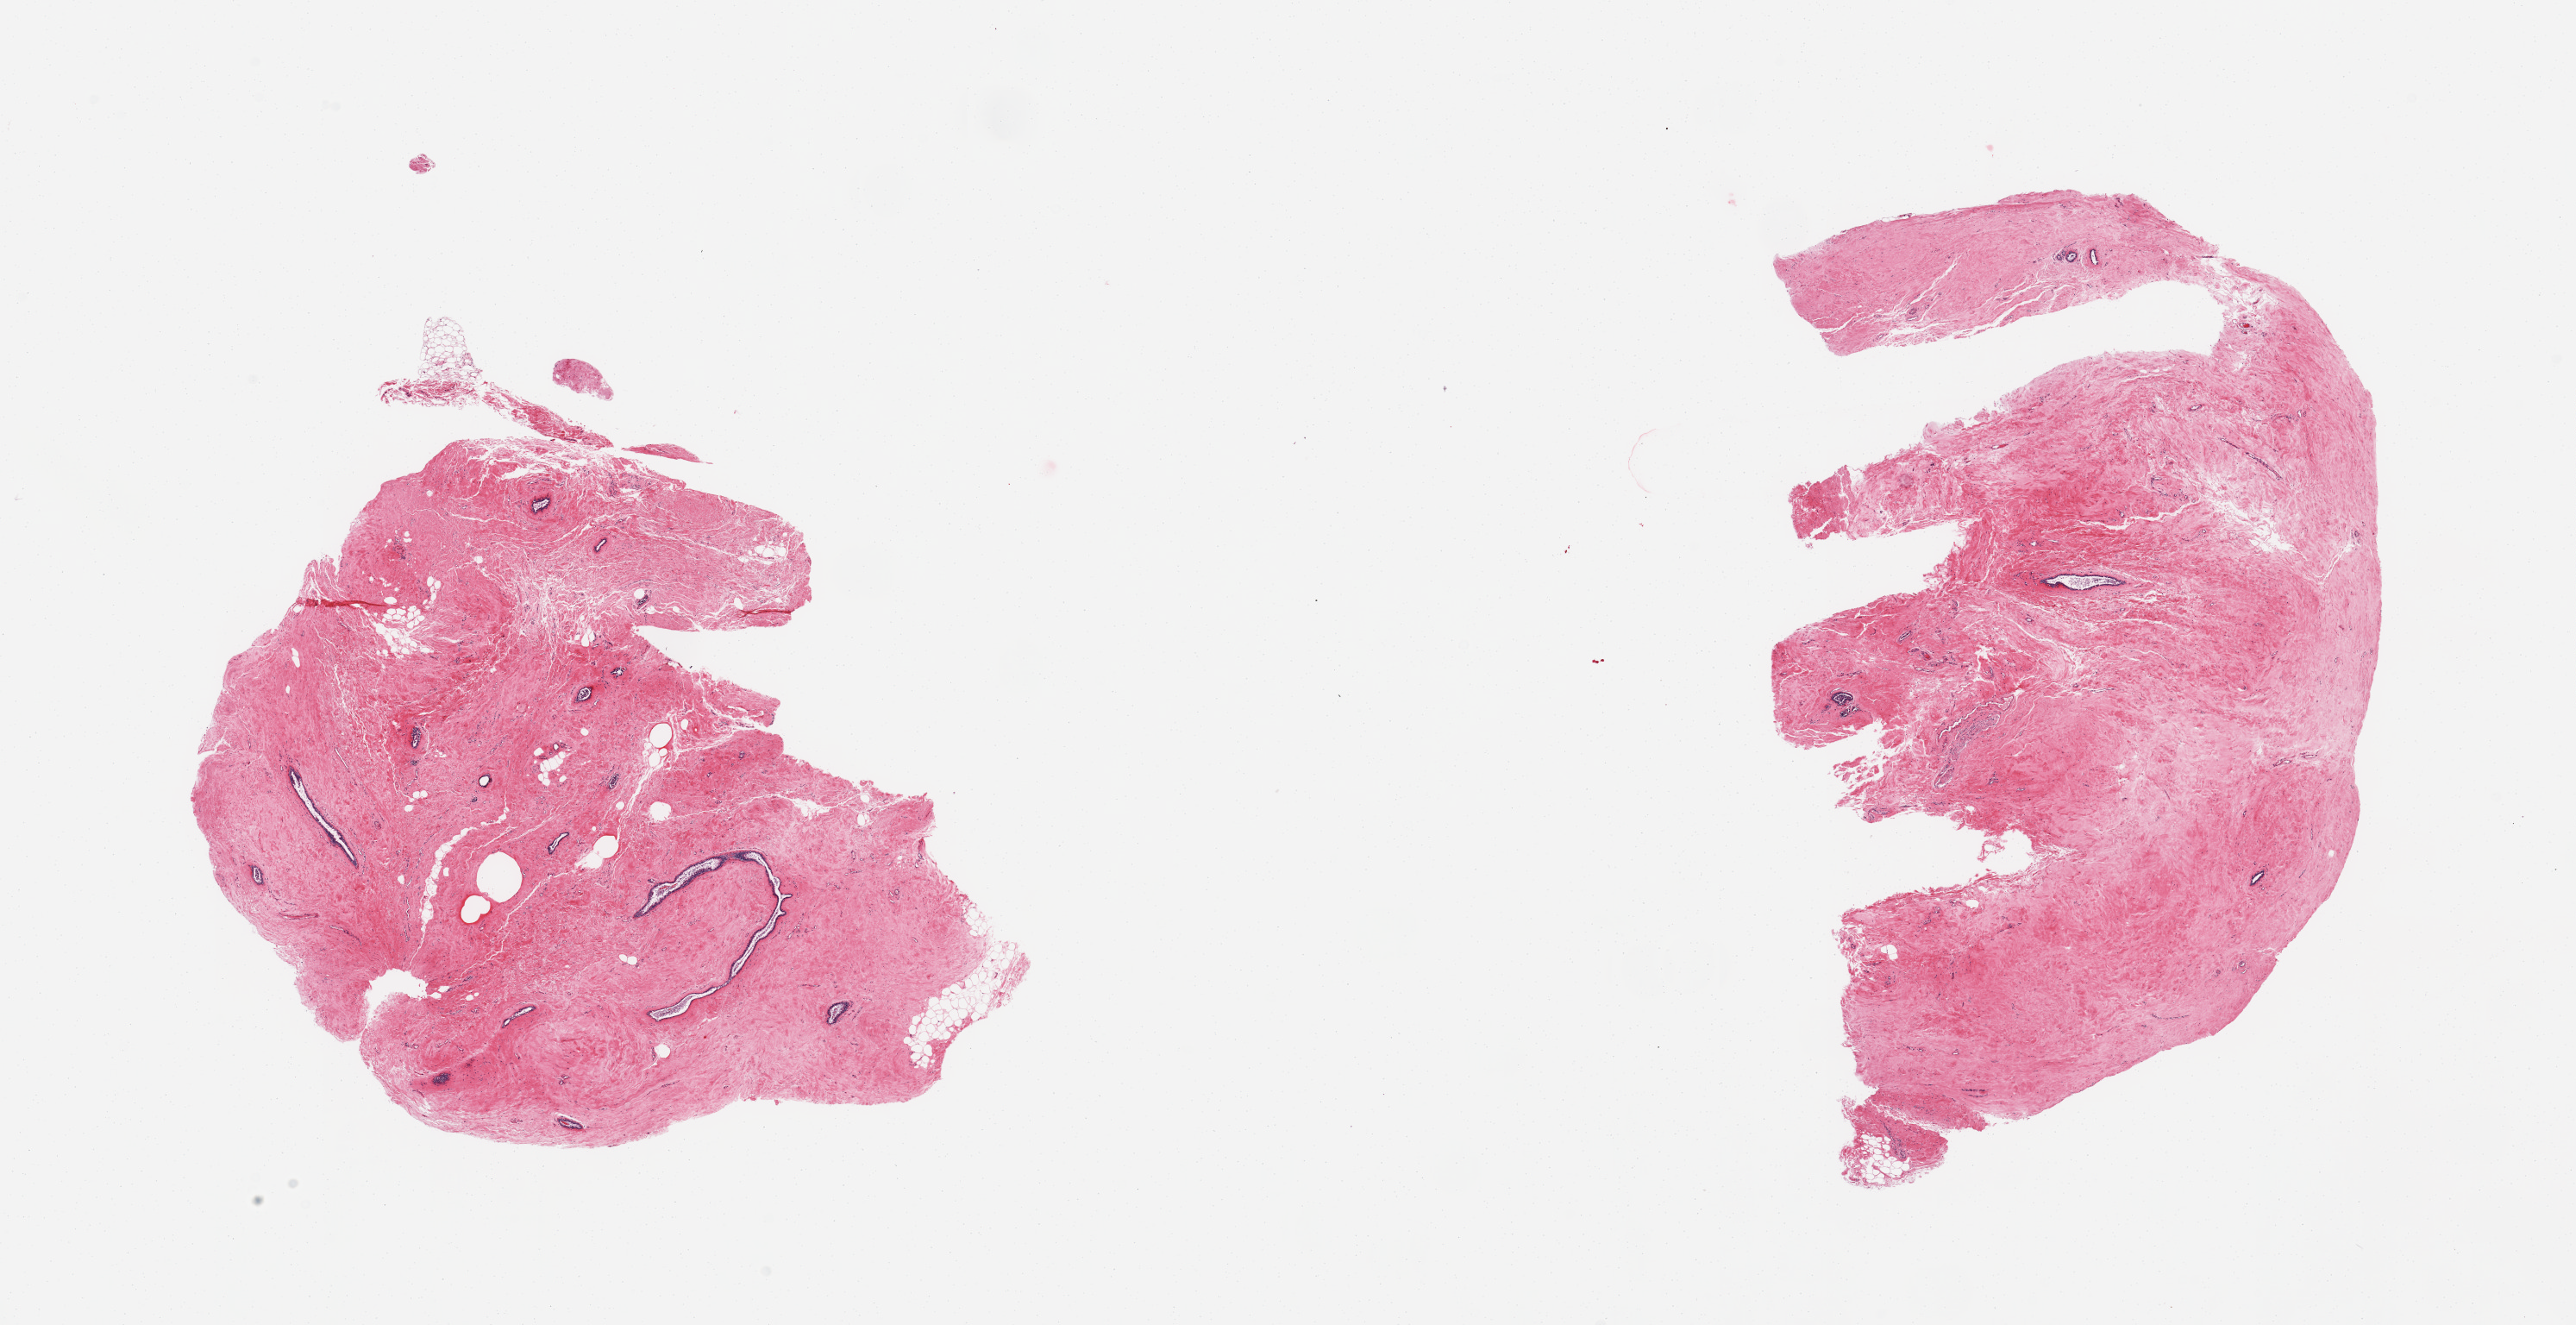
Digitized H&E-stained section, brightfield — whole scanned area (about 23.6 x 12.1 mm, acquisition: 20x scan) shown as a low-resolution overview; PAXgene-fixed paraffin-embedded (PFPE) section; section of breast (target tissue); tissue donor sample. Donor sex: male.
Reviewer comment on this tissue sample: 2 pieces, prominent stromal and ductal hyperplasia.